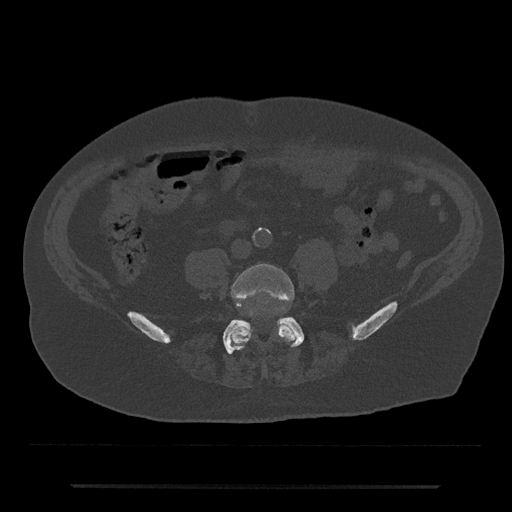
CT including the spine, one axial slice; position 320 of 797 along the scan axis; reconstruction kernel Br40s/3; 120 kVp; bone window (W 1800 / L 400 HU); 0.5 mm slice thickness; 512 × 512 image matrix, field of view 434 × 434 mm. Male patient, age 80 years. Case-level facts recorded for this patient, not image findings: primary cancer: prostate; vertebrae with lytic lesions (as recorded): L1, T11.
Structures marked on this image (semi-automatically segmented with operator editing):
- L4 vertebra: box from (x=229, y=264) to (x=297, y=349) px
- L5 vertebra: (x=223, y=313)–(x=304, y=354)